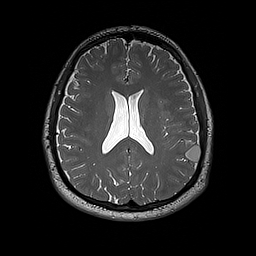
Brain MRI from a brain-tumour surgery series, one axial slice; position 83 of 192 along the scan axis; 1 mm slice thickness; 256 × 256 image matrix, field of view 250 × 250 mm. From the clinical record (not read from this slice): histopathology: Dysembryoplastic neuroepithelial tumor; WHO grade: 1; IDH mutation: no; tumour location: Left Inferior Parietal.
Structures marked on this image (manually delineated by an expert):
- tumour: bounding box (x1, y1, x2, y2) in pixels: (186, 146, 201, 162)